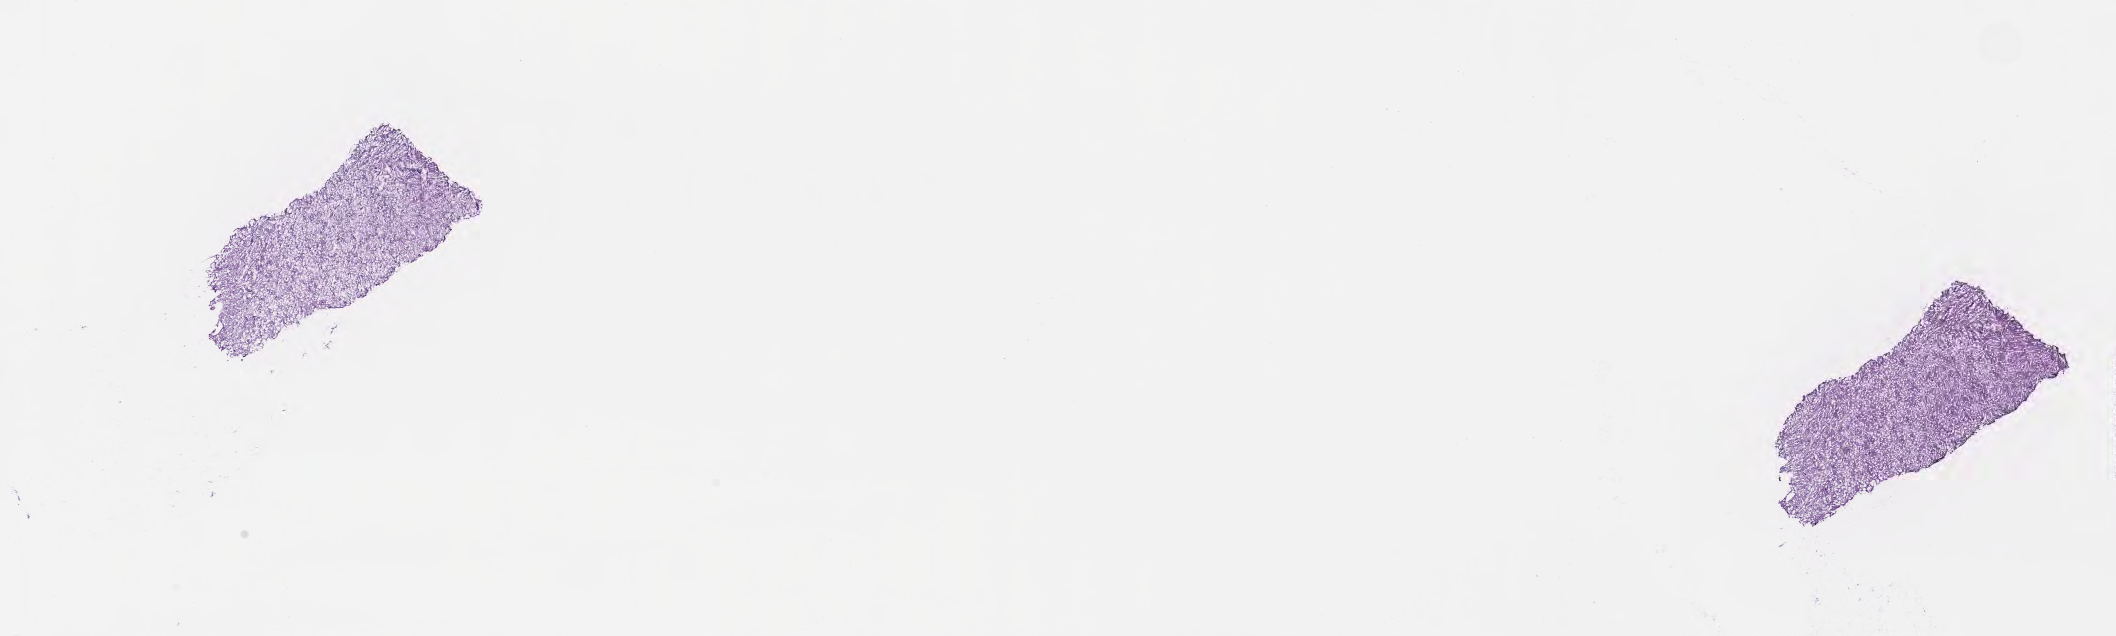
H&E whole-slide image — shown as a low-resolution overview of the whole scanned area (about 17.1 x 5.1 mm). Frozen section. Primary tumor. Site: brain. Male patient; age at initial diagnosis 68 years. Pathologist review of this section (percent, as recorded): tumor cells 33%, tumor nuclei 62%, stromal cells 47%, necrosis 0%, normal cells 20%. Inflammatory infiltration, as recorded: lymphocyte infiltration 0%, monocyte infiltration 0%, neutrophil infiltration 0%.
Section: top of the tissue portion. Diagnosis: Glioblastoma, NOS.